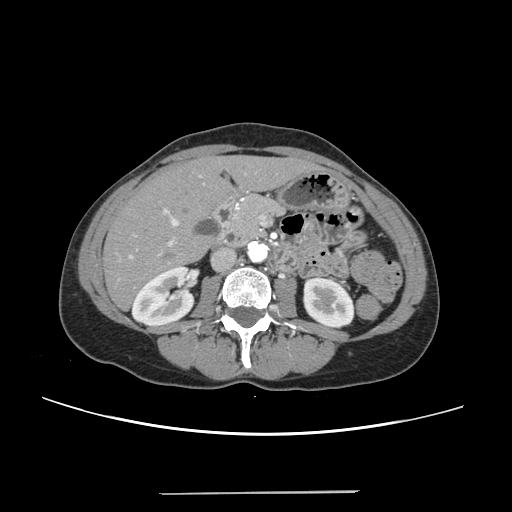
Contrast-enhanced abdominal CT, one axial slice; 120 kVp; intravenous contrast given; soft-tissue window (W 400 / L 40 HU); 512 × 512 image matrix, field of view 371 × 371 mm. Female patient, age 60 years. From the clinical record (not read from this slice): diagnosis: colorectal cancer liver metastases, imaged before liver resection; multiple liver metastases: no.
Structures marked on this image (manually delineated by an expert):
- liver: bounding box [x1, y1, x2, y2] px = [105, 157, 311, 308]
- planned liver remnant (the part of the liver to remain after resection): [105, 158, 313, 308]
- portal vein (with intrahepatic branches): [129, 175, 244, 269]